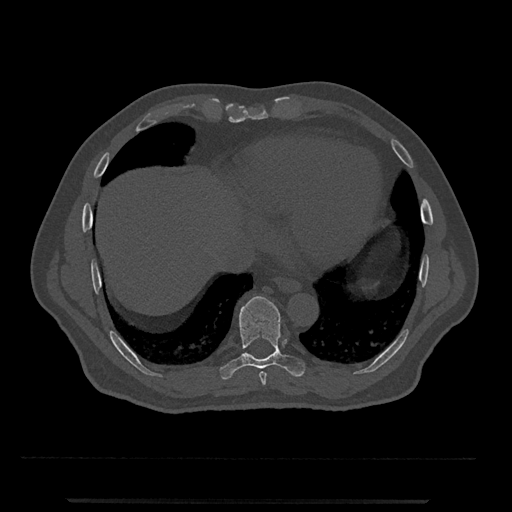
CT including the spine, one axial slice. Position 578 of 797 along the scan axis. Reconstruction kernel Br40s/3. 120 kVp. Bone window (W 1800 / L 400 HU). 0.5 mm slice thickness. 512 × 512 image matrix, field of view 419 × 419 mm. Patient: male, 63 years. From the clinical record (not read from this slice): primary cancer: prostate.
Outlined on this slice (semi-automatic segmentation, software-assisted and operator-edited):
- T8 vertebra: bounding box (x1, y1, x2, y2) in pixels: (259, 372, 267, 386)
- T9 vertebra: (220, 296, 305, 380)